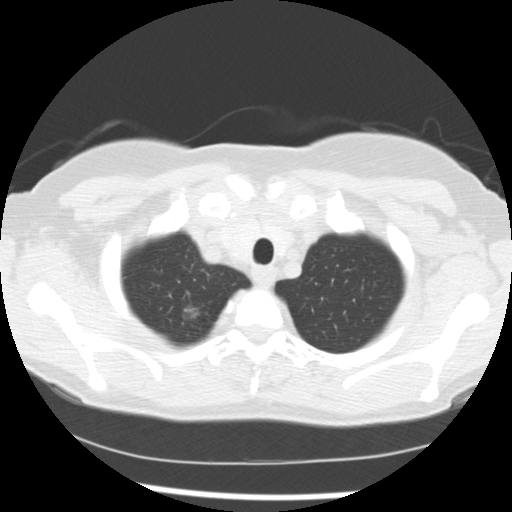
Axial slice from a low-dose chest CT screening exam. Baseline screening round. Lung window (W 1500 / L -600 HU). 2.5 mm slice thickness. Slice 22 of 241 in the series. 512 × 512 image matrix. Female participant, aged 60 years at enrolment.
Lesion marked by an expert reader, box from (x=169, y=293) to (x=209, y=330) px. The screening reader recorded 3 non-calcified nodules or masses ≥4 mm on this exam (right upper lobe, right middle lobe, left lower lobe); which of them this box marks is not recorded. Official screen result: positive, change unspecified: nodule(s) >= 4 mm or enlarging nodule(s), mass(es), or other non-specific abnormalities suspicious for lung cancer. Lung cancer was diagnosed 100 days after this screen: bronchiolo-alveolar adenocarcinoma, NOS, right upper lobe, moderately differentiated (G2), stage IA (AJCC 6th edition), 9 mm at pathology.